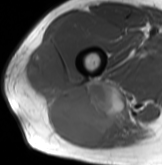
MRI of an extremity soft-tissue mass, one axial slice. Position 61 of 61 along the scan axis. MR volume resampled by the dataset authors to the PET/CT grid (not the native acquisition matrix). 3.27 mm slice thickness. 162 × 165 image matrix, field of view 158 × 161 mm. Male patient. From the clinical record (not read from this slice): histological type: poorly differentiated synovial sarcoma; grade: high; site of the primary tumour: right buttock.
Annotated regions visible in this slice (expert contour drawn on MRI and transferred to this co-registered scan by the dataset authors):
- gross tumour volume including surrounding oedema: bounding box (x1, y1, x2, y2) in pixels: (25, 43, 140, 146)
- gross tumour volume (mass): (25, 43, 126, 144)